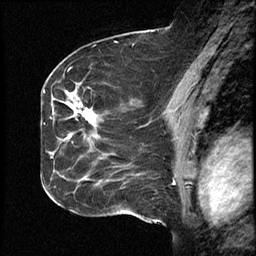
Breast MRI (dynamic contrast-enhanced), one sagittal slice; position 27 of 46 along the scan axis; dynamic contrast-enhanced study with each time point stored as its own series, time point 2 of 4 at this slice position (early post-contrast, ordered by acquisition time); 1.5 T; TE 4.2 ms, TR 18.3 ms; 3 mm slice thickness; 256 × 256 image matrix, field of view 200 × 200 mm. From the clinical record (not read from this slice): setting: breast cancer imaged before/during neoadjuvant chemotherapy; receptor status: HR-positive, HER2-negative.
Outlined on this slice (semi-automatically segmented with operator editing):
- analysis volume of interest (the breast-tissue region the enhancement analysis was run in; not a lesion): bounding box <64,71,111,195> (left, top, right, bottom; pixels)
- tumour enhancement mask (voxels above the 100 % enhancement threshold inside the analysis volume of interest): <80,104,94,122>